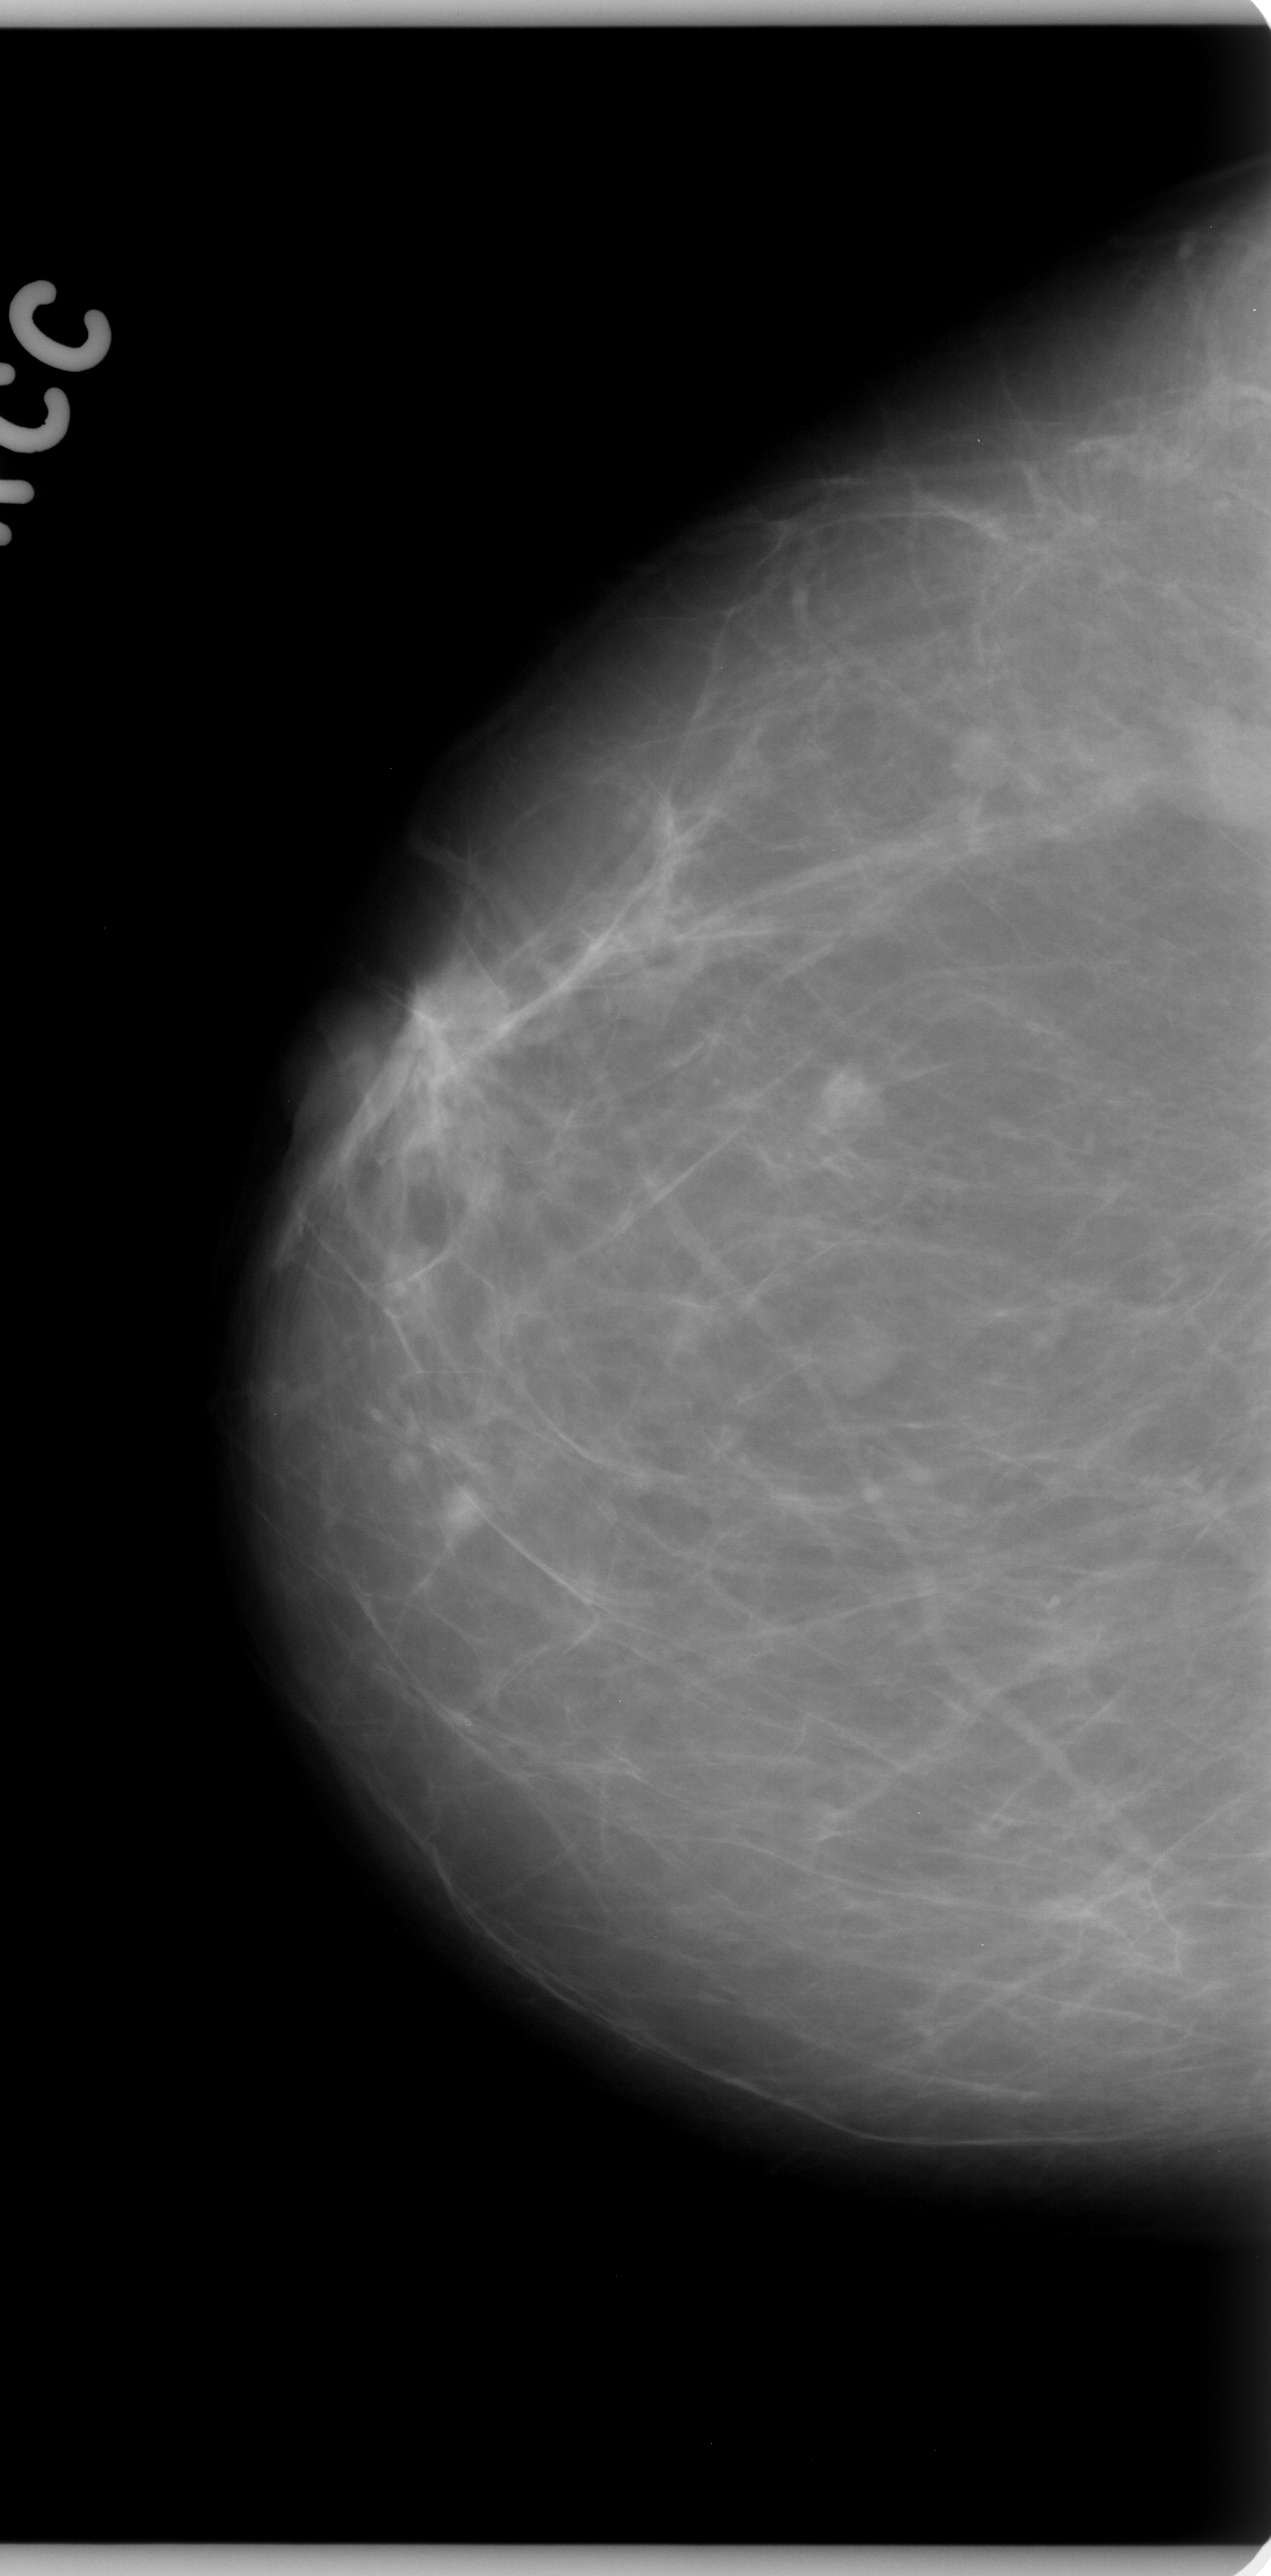
Digitized screen-film mammogram, right breast, CC view, breast composition: almost entirely fatty (BI-RADS density category 1 of 4).
Radiologist-marked abnormalities on this image: mass, shape oval, margins spiculated; BI-RADS assessment category 5; subtlety rating 5 on a 1 (subtle) to 5 (obvious) scale; pathology result (as recorded, not read from the image): malignant.